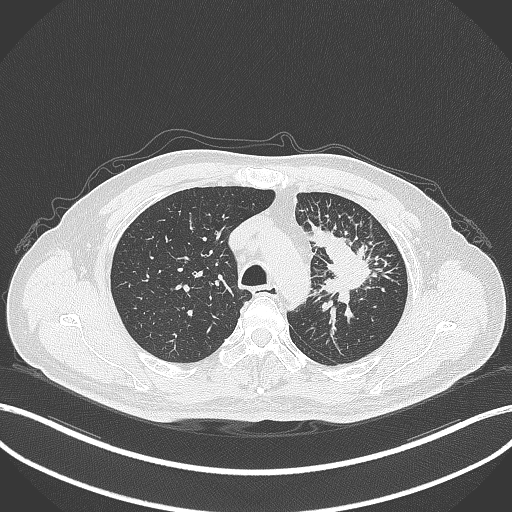
Chest CT, one axial slice; slice 269 of 386 in the series (ordered by position); reconstruction kernel B70f; 120 kVp; lung window (W 1500 / L -600 HU); 1 mm slice thickness; 512 × 512 image matrix. Patient: male, 69 years. Case-level facts recorded for this patient, not image findings: clinical TNM (as recorded): T2a N2 M0.
Outlined on this slice (bounding box drawn by a radiologist):
- lung tumour (recorded histology: adenocarcinoma): box from (x=308, y=220) to (x=381, y=306) px